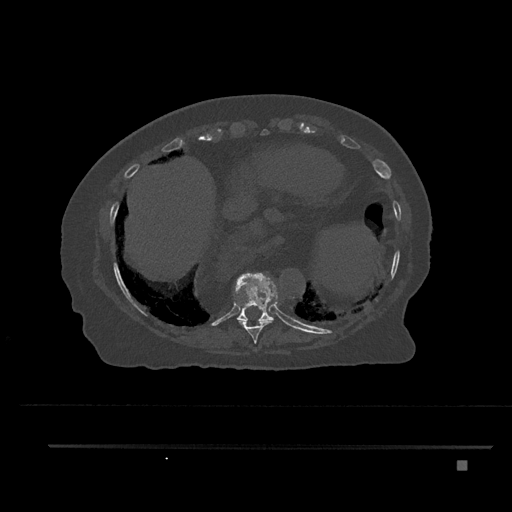
CT including the spine, one axial slice. Position 378 of 797 along the scan axis. 120 kVp. Bone window (W 1800 / L 400 HU). 0.5 mm slice thickness. 512 × 512 image matrix, field of view 437 × 437 mm. Patient: female, 76 years. From the clinical record (not read from this slice): primary cancer: lung.
Annotated regions visible in this slice (semi-automatically segmented with operator editing):
- T10 vertebra: bounding box [x1, y1, x2, y2] px = [235, 273, 275, 323]
- T9 vertebra: [235, 282, 271, 344]